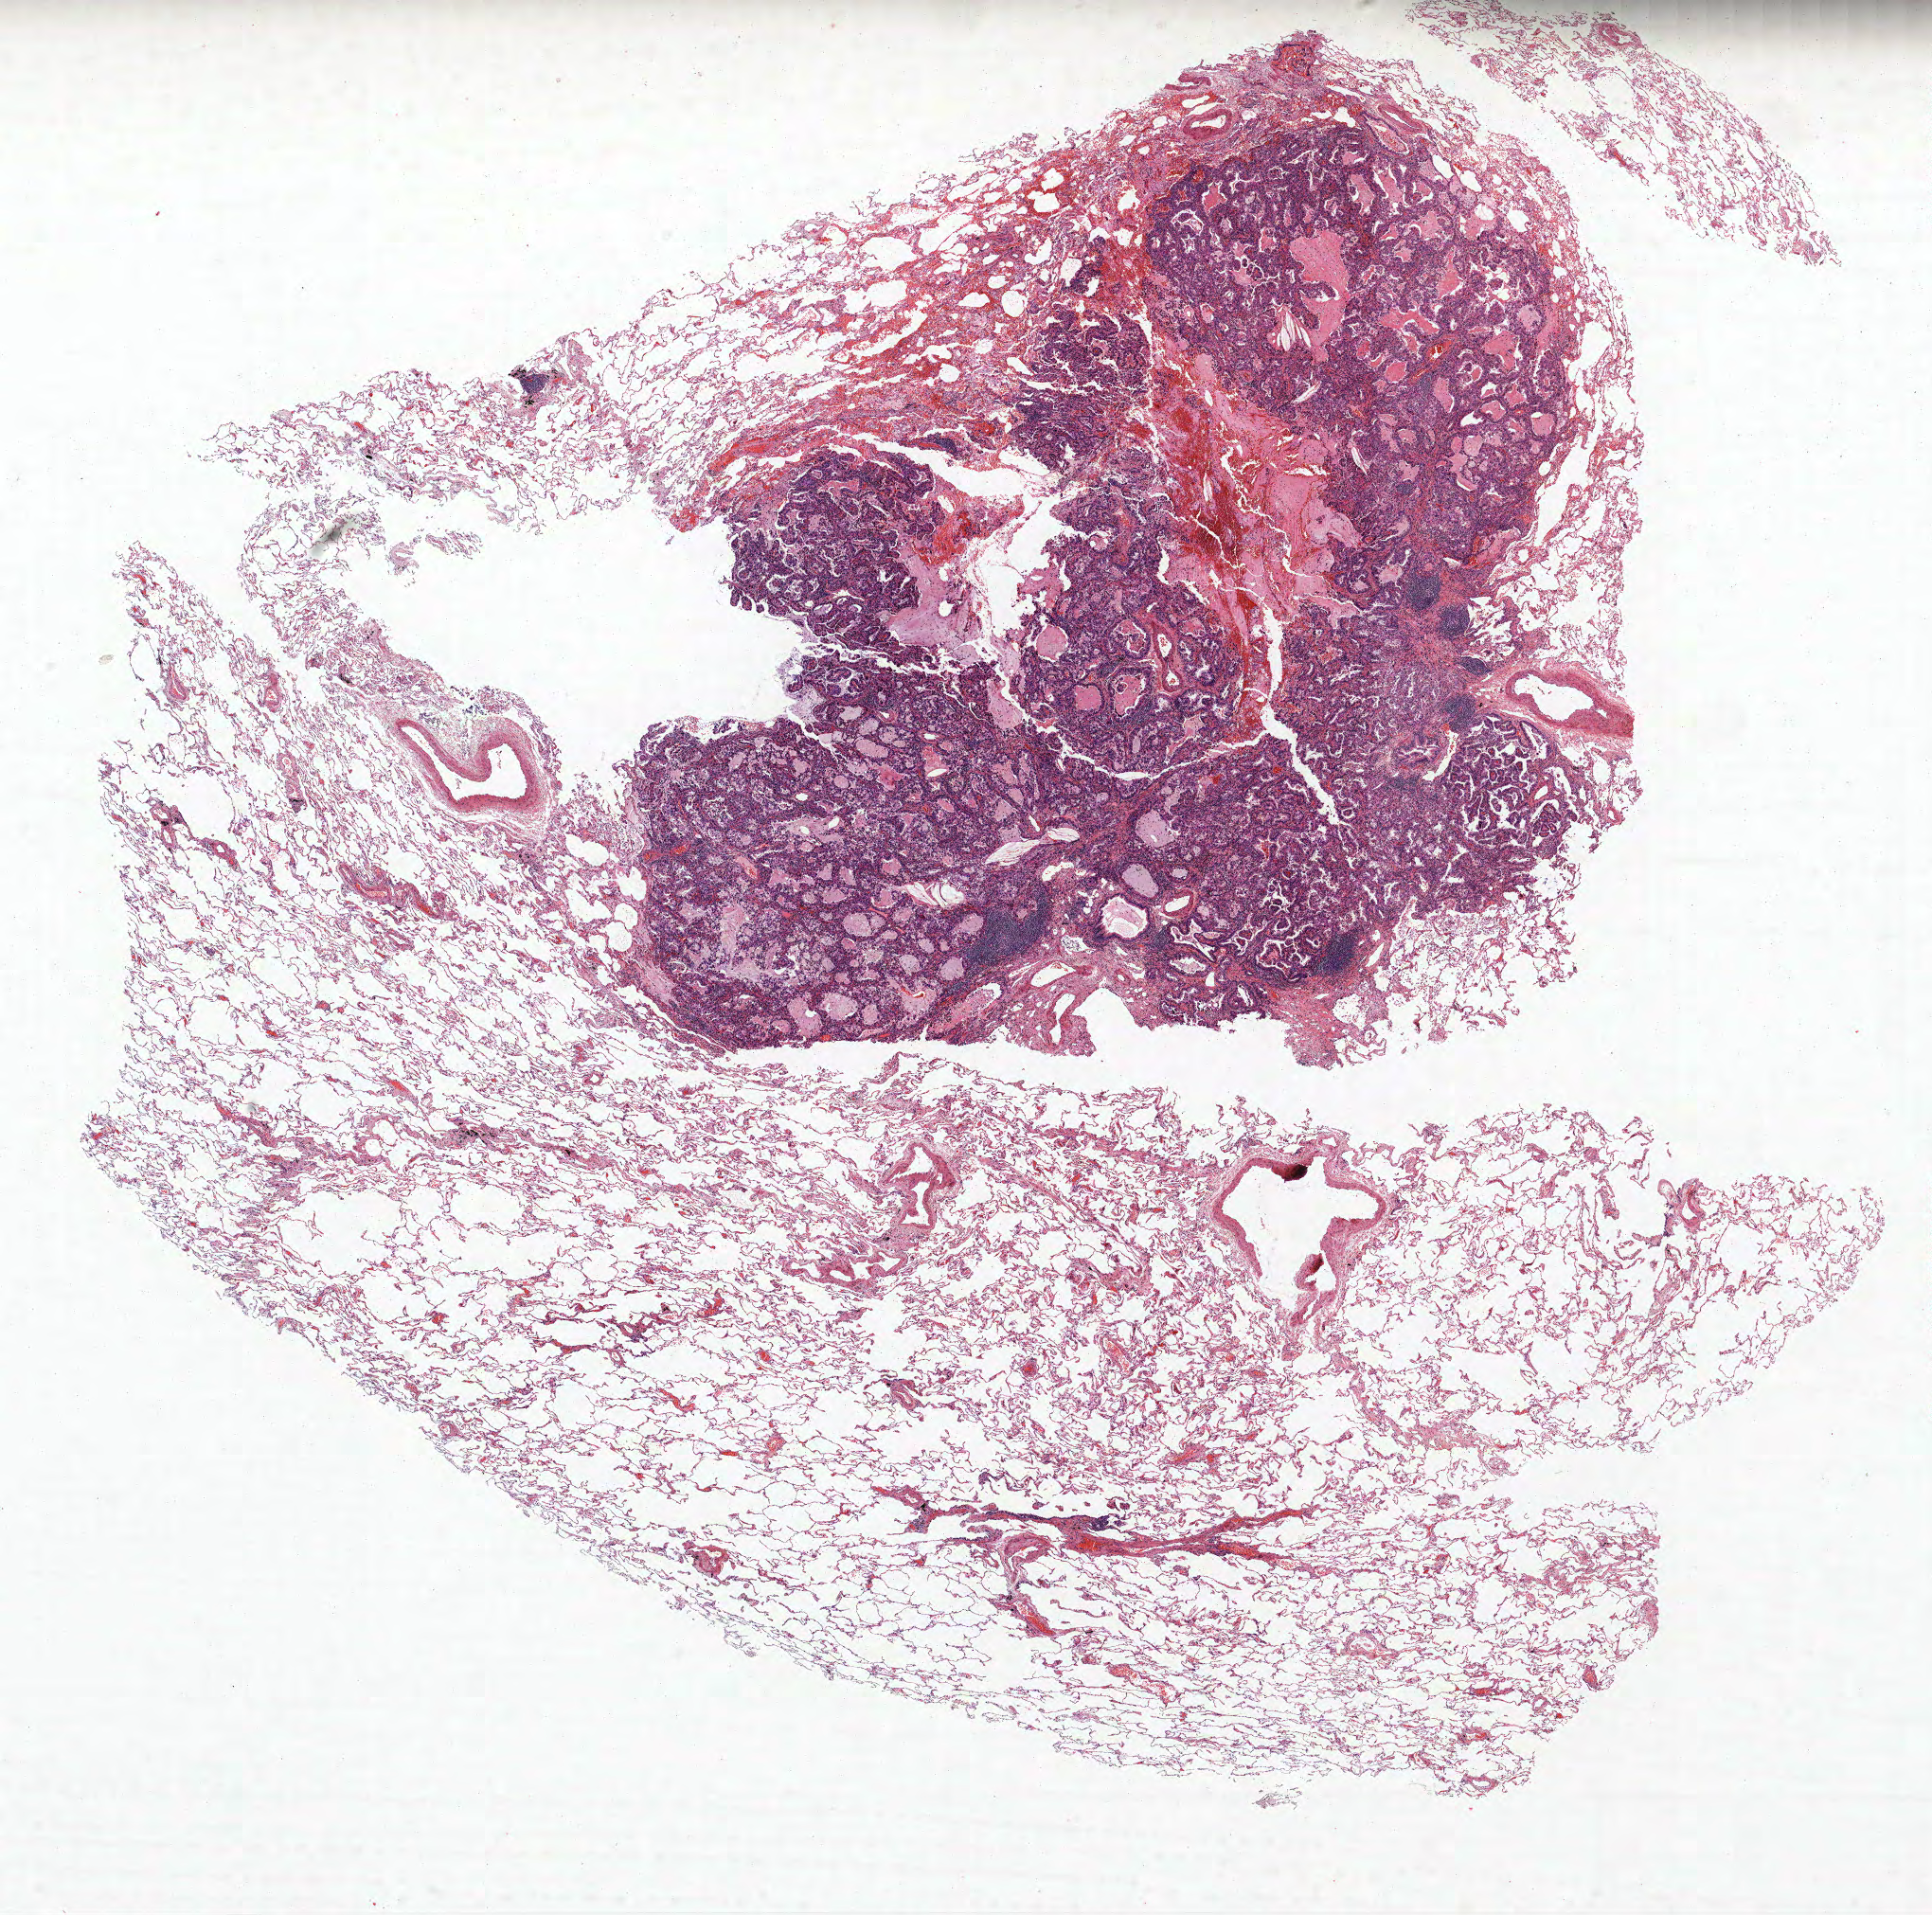
H&E whole-slide image, low-resolution overview of the scanned area, about 16.3 x 16.2 mm; FFPE section; lung. Male patient, aged 65 at enrolment. Former smoker at enrolment. Grade: moderately differentiated (G2).
- tumour size (pathology): 11 mm
- stage (AJCC 6th edition): IA
- primary tumour location (clinical record): right upper lobe
- participant's lung-cancer diagnosis: Adenocarcinoma, NOS (ICD-O-3 8140/3)